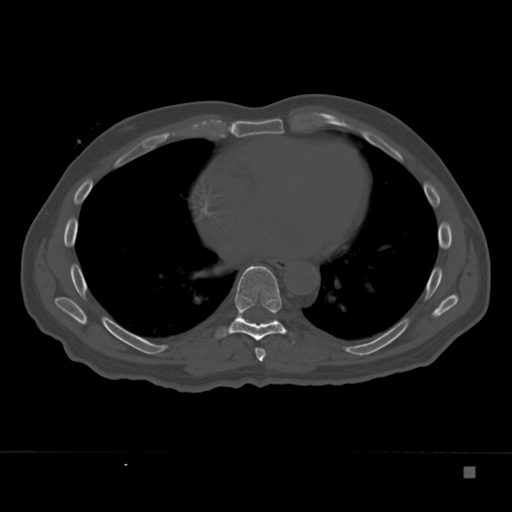
CT including the spine, one axial slice; position 207 of 332 along the scan axis; bone window (W 1800 / L 400 HU); 1.5 mm slice thickness; 512 × 512 image matrix. Male patient, age 72 years. From the clinical record (not read from this slice): primary cancer: skeletal.
Annotated regions visible in this slice (semi-automatically segmented with operator editing):
- T7 vertebra: bounding box (x1, y1, x2, y2) in pixels: (255, 348, 266, 362)
- T8 vertebra: (216, 266, 287, 341)